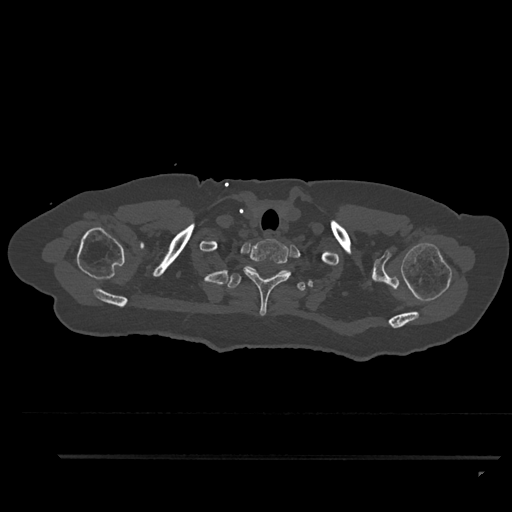
CT including the spine, one axial slice. Position 752 of 797 along the scan axis. Reconstruction kernel Br40s/3. Bone window (W 1800 / L 400 HU). 0.5 mm slice thickness. 512 × 512 image matrix, field of view 408 × 408 mm. Patient: female, 44 years. Case-level facts recorded for this patient, not image findings: primary cancer: renal; vertebrae with lytic lesions (as recorded): L1.
Structures marked on this image (semi-automatic segmentation, software-assisted and operator-edited):
- T1 vertebra: bounding box [x1, y1, x2, y2] px = [244, 239, 291, 316]
- T2 vertebra: [227, 273, 306, 291]